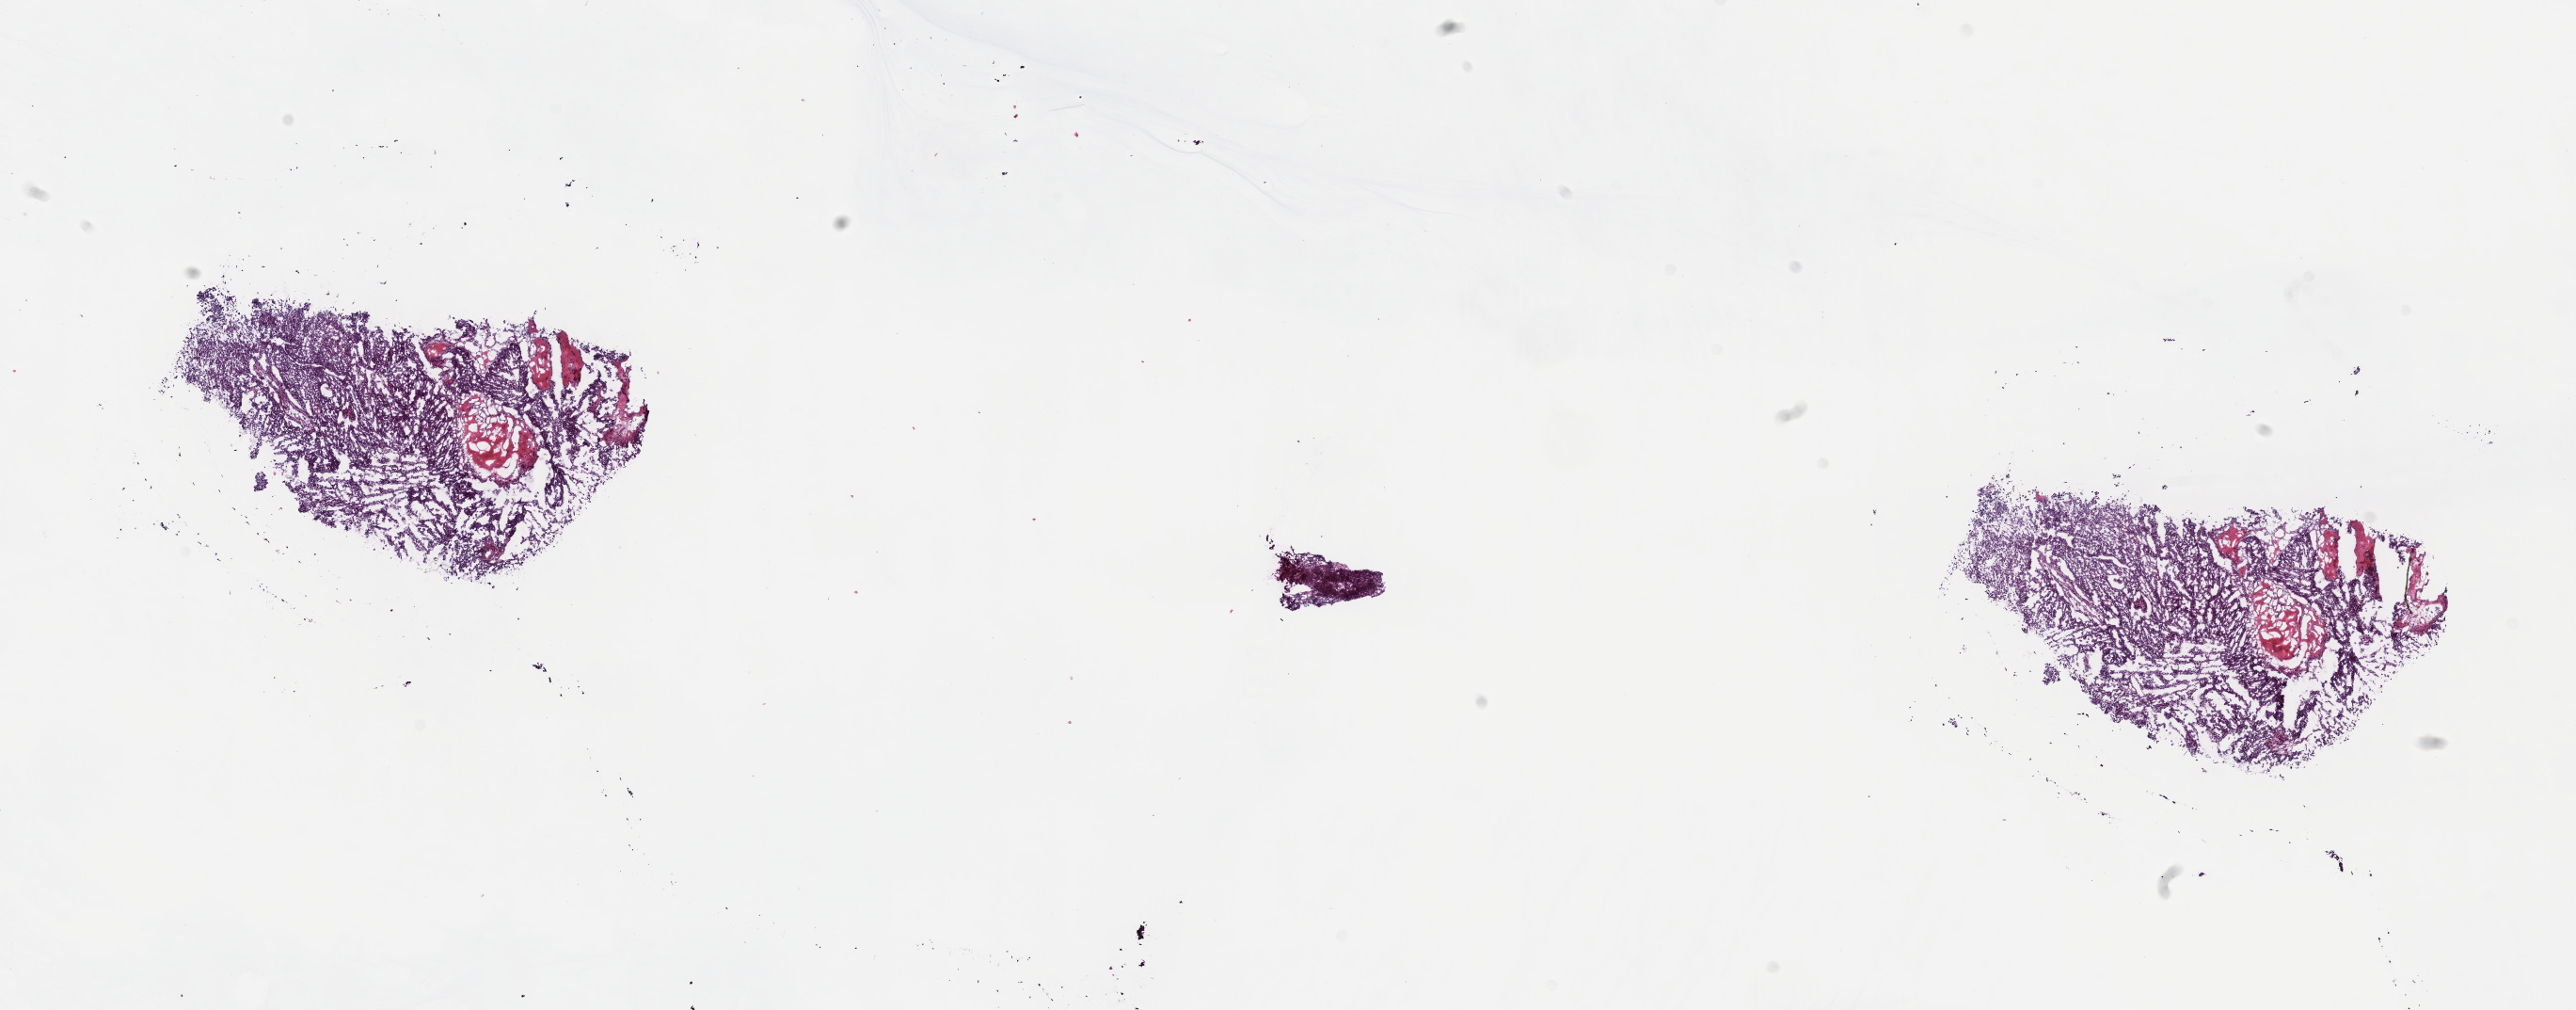
H&E-stained whole-slide image, a low-resolution overview of the entire scanned area, about 22.1 x 8.7 mm (acquisition: 40x scan), frozen section from the top of the tissue portion, primary tumour sample from the bladder. Patient: male, age at initial diagnosis 75 years.
Diagnosis: Papillary transitional cell carcinoma.